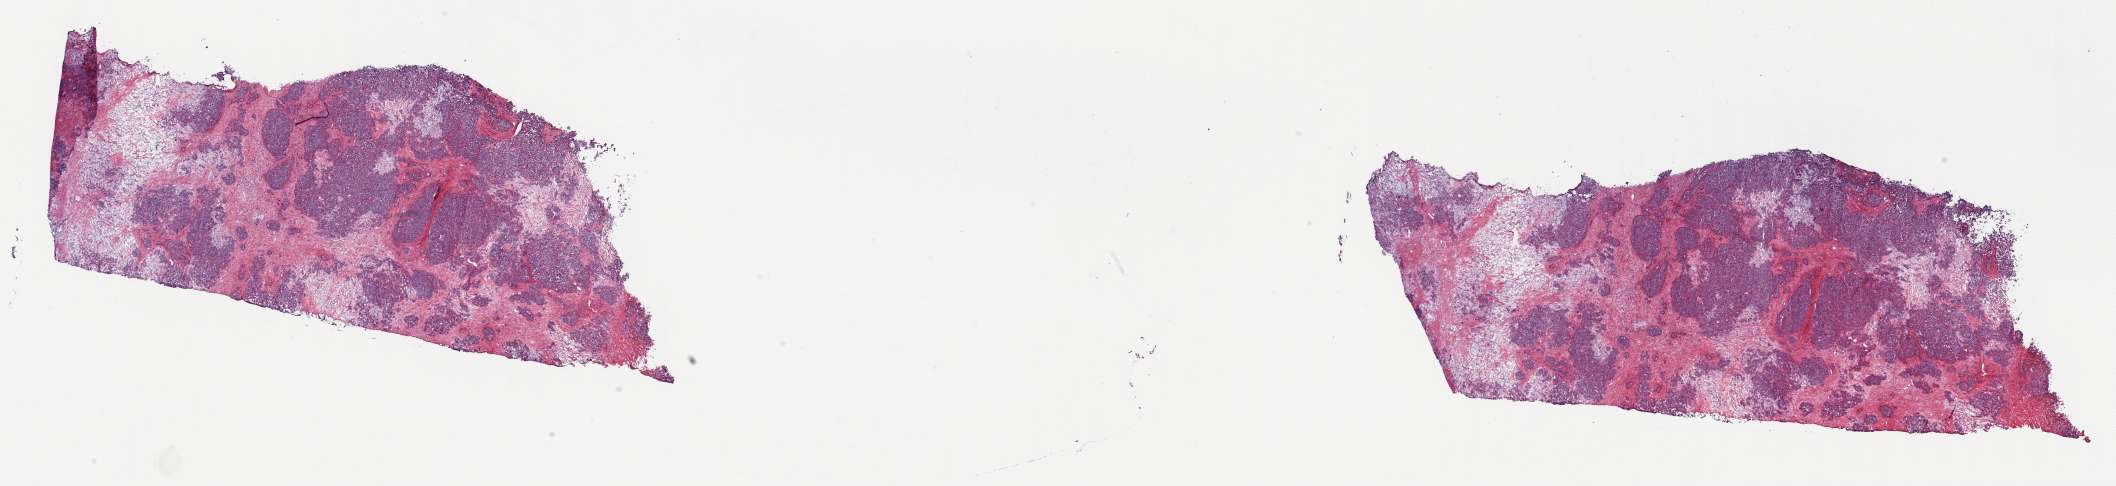
Digitized H&E tissue section (whole slide) — a low-resolution overview of the entire scanned area, about 34.2 x 7.9 mm (from a 40x scan), frozen section, primary tumour sample from the bile duct. Female, age 31 years at initial diagnosis. Histologic grade: G3 (poorly differentiated). Slide review estimates, as recorded: tumour cells 45%, tumour nuclei 90%, normal cells 0%, stromal cells 54%, necrosis 1%. Infiltration values recorded for this section: lymphocyte infiltration 5%, monocyte infiltration 1%, neutrophil infiltration 1%.
* AJCC pathologic stage: IVA (7th edition)
* pathologic diagnosis: Cholangiocarcinoma (intrahepatic bile duct)